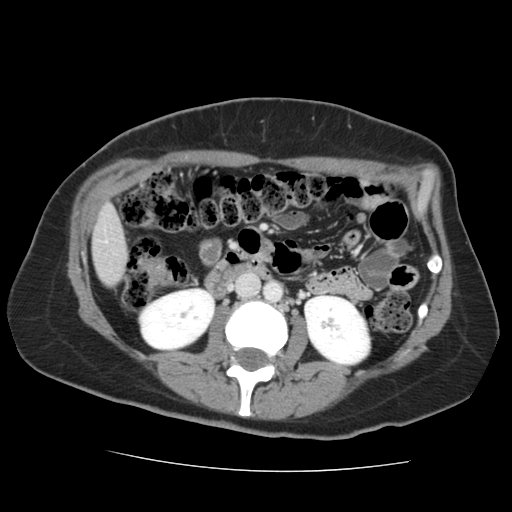
Contrast-enhanced abdominal CT, one axial slice. Position 47 of 144 along the scan axis. 120 kVp. Soft-tissue window (W 400 / L 40 HU). 2.5 mm slice thickness. 512 × 512 image matrix. Female patient, age 46 years. Case-level facts recorded for this patient, not image findings: diagnosis: colorectal cancer liver metastases, imaged before liver resection; multiple liver metastases: no; largest metastasis: 2.8 cm; chemotherapy before resection: yes.
Structures marked on this image (expert manual segmentation):
- liver: bounding box [x1, y1, x2, y2] px = [93, 208, 127, 286]
- planned liver remnant (the part of the liver to remain after resection): [95, 208, 120, 231]